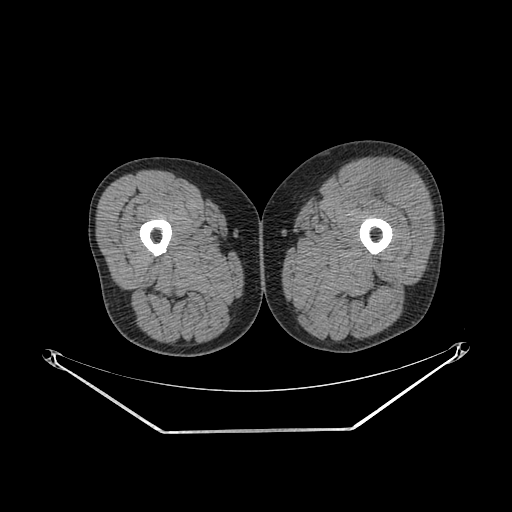
CT of an extremity soft-tissue mass (from a PET/CT study), one axial slice; position 223 of 267 along the scan axis; reconstruction kernel SOFT; soft-tissue window (W 400 / L 40 HU); 3.75 mm slice thickness; 512 × 512 image matrix. Male patient. From the clinical record (not read from this slice): histological type: extraskeletal osteosarcoma; grade: high; site of the primary tumour: thigh.
Annotated regions visible in this slice (expert contour drawn on MRI and transferred to this co-registered scan by the dataset authors):
- gross tumour volume (mass): box from (x=372, y=169) to (x=414, y=204) px